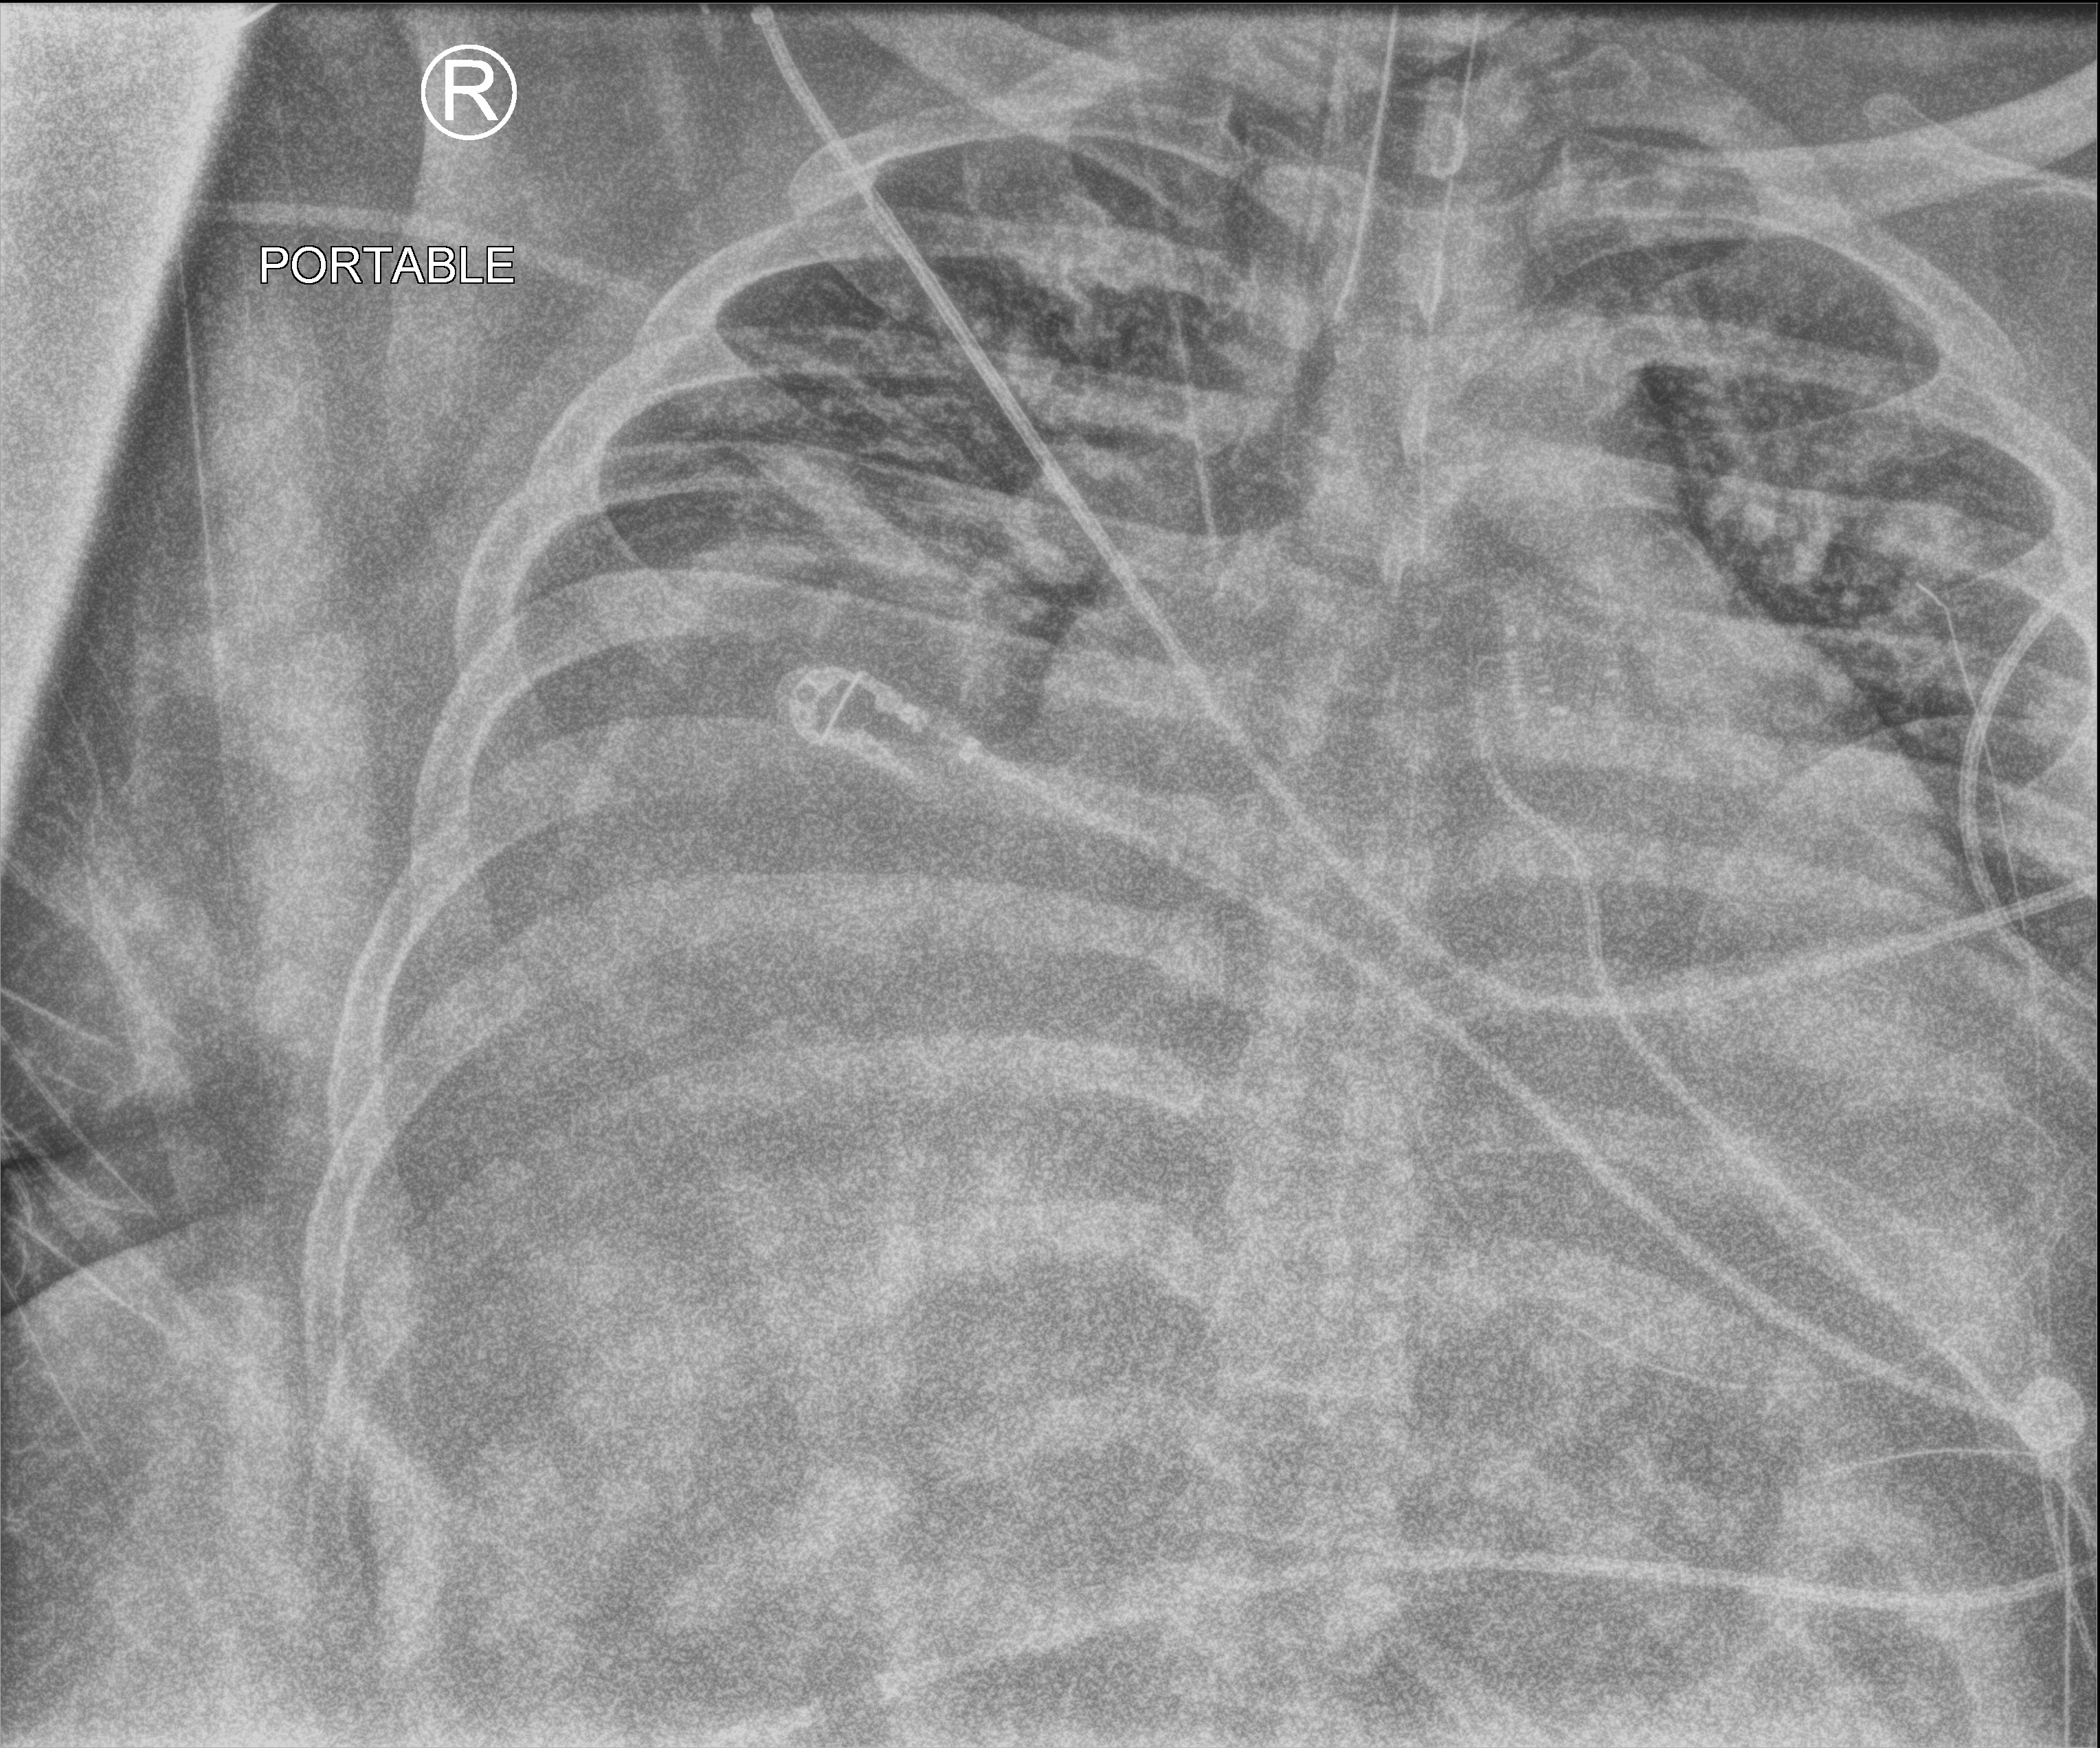
Bedside chest radiograph (computed radiography); anteroposterior (AP) projection. Patient hospitalised with COVID-19; male, aged 18–59 years.
Admission-level facts for this patient (not findings on this image; timing relative to this image not recorded): mechanically ventilated during this hospital stay: yes.